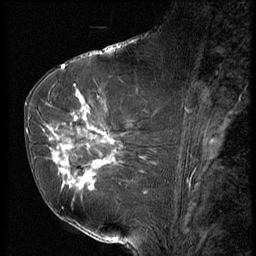
Breast MRI (dynamic contrast-enhanced), one sagittal slice; position 31 of 56 along the scan axis; 3 images stored at this slice position (order not interpretable as contrast timing); 1.5 T; TE 4.2 ms, TR 9 ms; 256 × 256 image matrix. Female patient, age 61 years. From the clinical record (not read from this slice): setting: breast cancer imaged before/during neoadjuvant chemotherapy; receptor status: HR-positive, HER2-negative.
Structures marked on this image (semi-automatic segmentation, software-assisted and operator-edited):
- analysis volume of interest (the breast-tissue region the enhancement analysis was run in; not a lesion): bounding box <47,89,153,191> (left, top, right, bottom; pixels)
- tumour enhancement mask (voxels above the 140 % enhancement threshold inside the analysis volume of interest): <48,95,116,189>